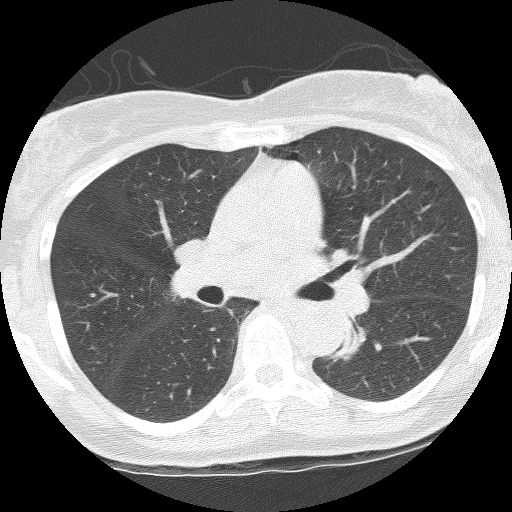
Low-dose screening chest CT, axial slice. Third screening round (two years after baseline). Lung window (W 1500 / L -600 HU). 2.5 mm slice thickness. 512 × 512 image matrix. Female, age 62 years at enrolment. Former smoker at enrolment.
Expert reader's lesion annotation, bounding box (x1, y1, x2, y2) in pixels: (324, 317, 381, 360). The screening reader recorded 3 non-calcified nodules or masses ≥4 mm on this exam (right upper lobe, left lower lobe, left upper lobe); which of them this box marks is not recorded. Official screen result: positive, other. Lung cancer was diagnosed 165 days after this screen: squamous cell carcinoma, NOS, left lower lobe, stage IIIB (AJCC 6th edition), 31 mm at pathology.